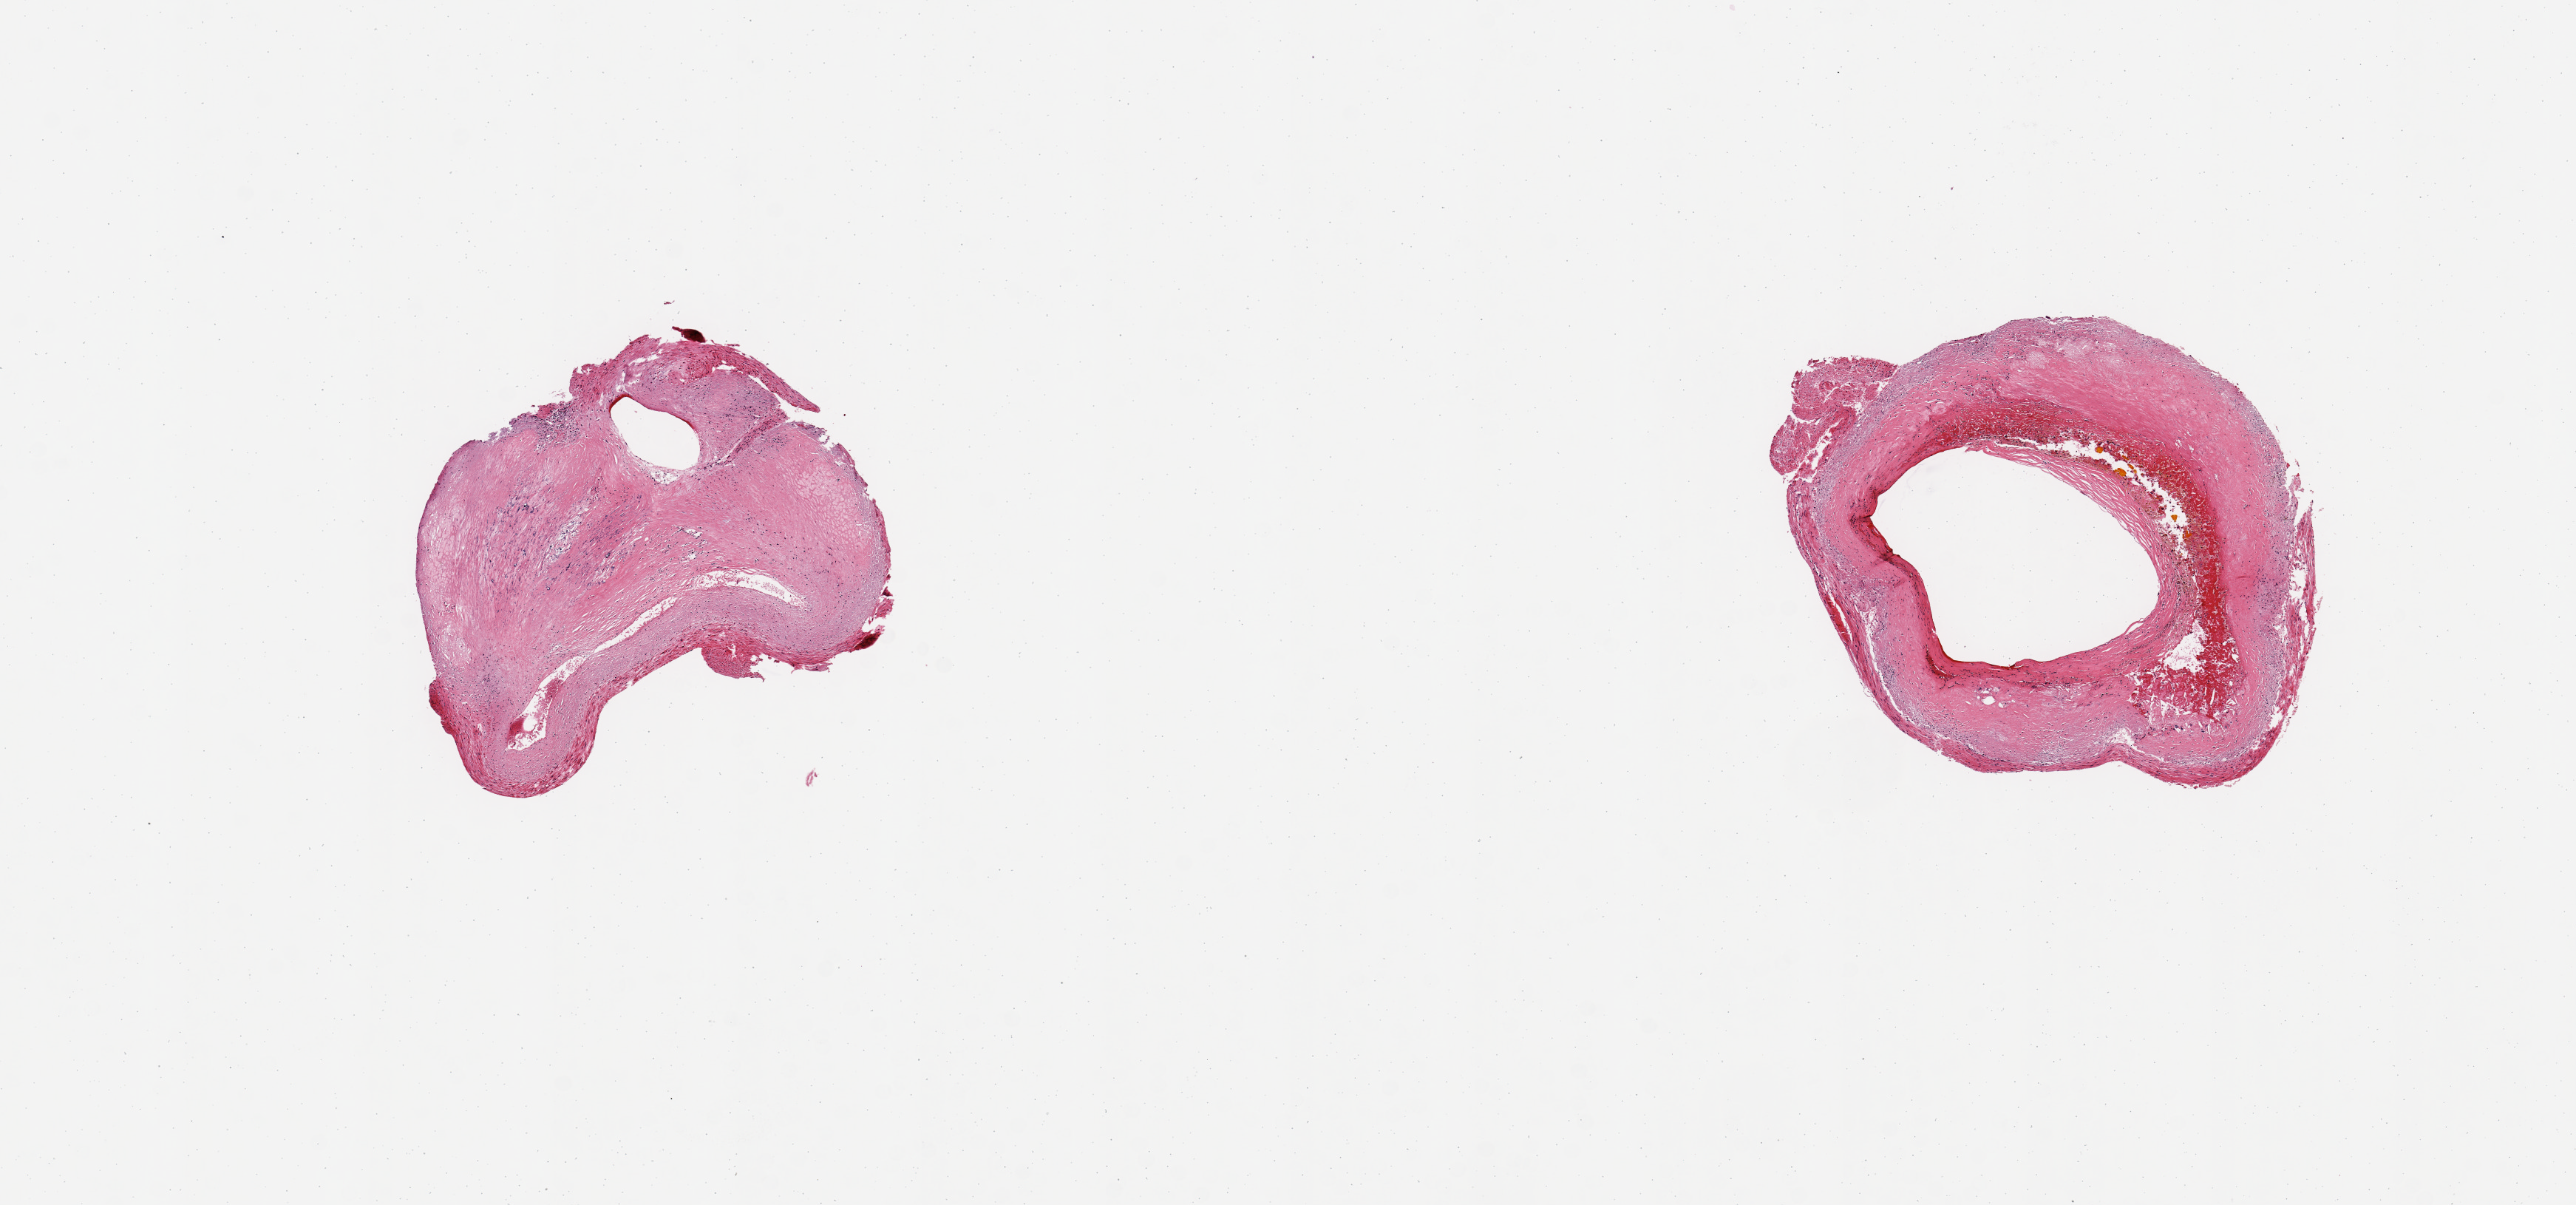
Digitized H&E-stained section, whole scanned area (about 13.8 x 6.4 mm, from a 20x scan) shown as a low-resolution overview; PAXgene-fixed, paraffin-embedded tissue; target tissue: coronary artery; tissue donor sample. Male donor.
* review note (as recorded): 2aliquots, ~2.5mm d. Subtotally occlusive atheroscerosis